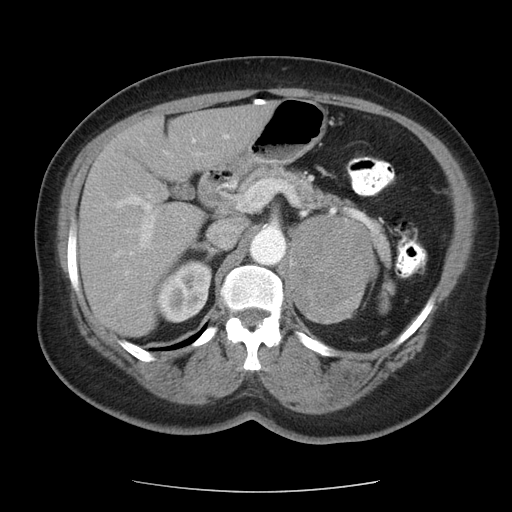
Contrast-enhanced abdominal CT, one axial slice. Position 67 of 95 along the scan axis. 120 kVp. Intravenous contrast given. Soft-tissue window (W 400 / L 40 HU). 5 mm slice thickness. 512 × 512 image matrix, field of view 362 × 362 mm. Female patient, age 71 years. From the clinical record (not read from this slice): diagnosis: adrenocortical carcinoma; tumour side: left adrenal.
Outlined on this slice (semi-automatic segmentation, software-assisted and operator-edited):
- mass: bounding box (x1, y1, x2, y2) in pixels: (289, 216, 374, 322)